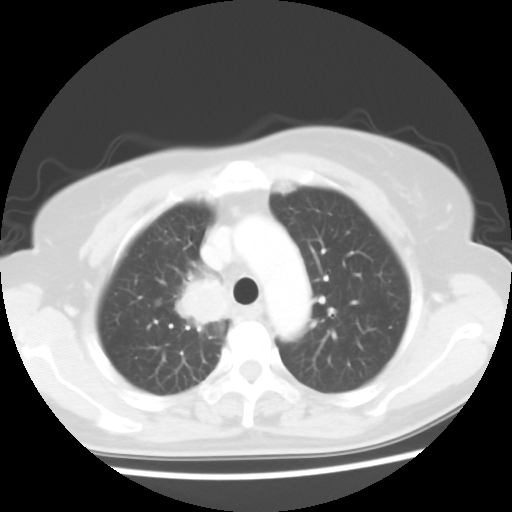
Chest CT, one axial slice. Slice 43 of 56 in the series (ordered by position). Reconstruction kernel STANDARD. 120 kVp. Lung window (W 1500 / L -600 HU). 5 mm slice thickness. 512 × 512 image matrix, field of view 314 × 314 mm. Patient: female, 62 years. Case-level facts recorded for this patient, not image findings: clinical TNM (as recorded): T2 N1 M1a.
Outlined on this slice (rectangle marked by the reading radiologist):
- lung tumour (recorded histology: adenocarcinoma): bounding box [x1, y1, x2, y2] px = [166, 268, 244, 342]